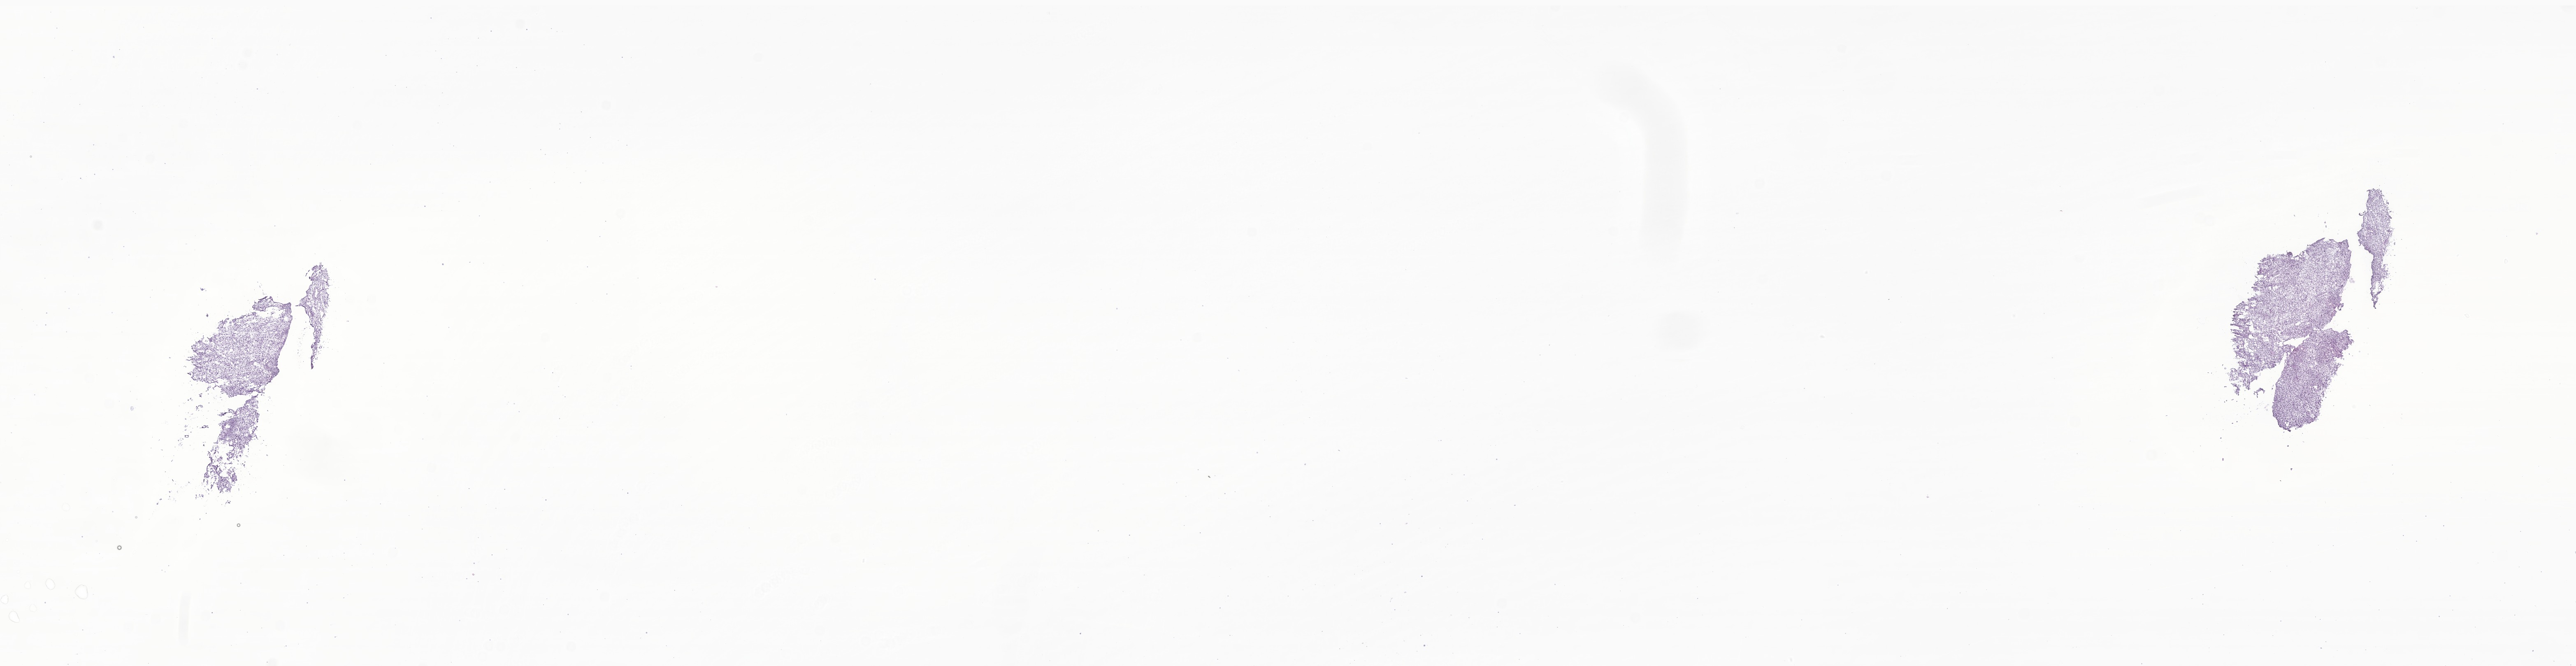
Digitized H&E-stained section of tumor tissue from the mandible — whole scanned area (about 26.4 x 6.8 mm) shown as a low-resolution overview. Cryosection (OCT / tissue freezing medium). Patient: male, age 65 months.
Recorded diagnosis: Rhabdomyosarcoma, NOS.